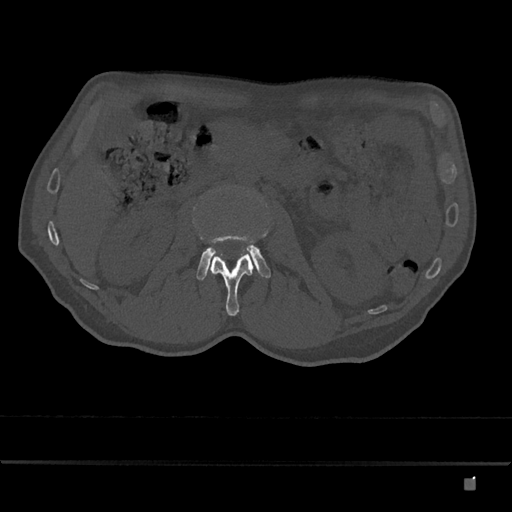
CT including the spine, one axial slice; slice 450 of 797 in the series (ordered by position); bone window (W 1800 / L 400 HU); 0.5 mm slice thickness; 512 × 512 image matrix, field of view 390 × 390 mm. Male patient, age 72 years. From the clinical record (not read from this slice): primary cancer: prostate.
Annotated regions visible in this slice (semi-automatic segmentation, software-assisted and operator-edited):
- L2 vertebra: bounding box [x1, y1, x2, y2] px = [209, 234, 253, 316]
- L3 vertebra: [197, 245, 271, 280]